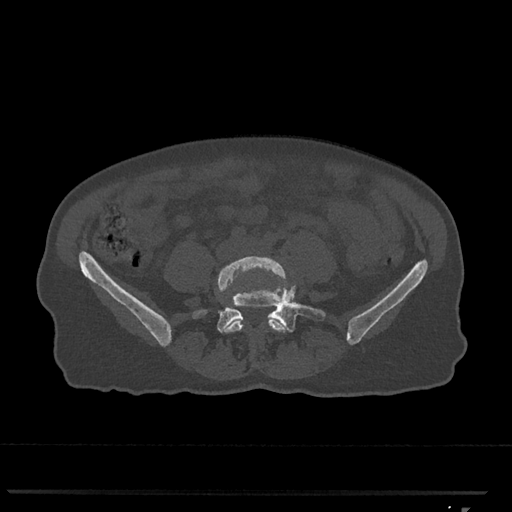
CT including the spine, one axial slice; position 174 of 793 along the scan axis; reconstruction kernel Br40s/3; 120 kVp; bone window (W 1800 / L 400 HU); 512 × 512 image matrix, field of view 380 × 380 mm. Female patient, age 62 years. From the clinical record (not read from this slice): primary cancer: renal.
Structures marked on this image (semi-automatic segmentation, software-assisted and operator-edited):
- L4 vertebra: bounding box (x1, y1, x2, y2) in pixels: (217, 256, 288, 333)
- L5 vertebra: (193, 271, 326, 333)